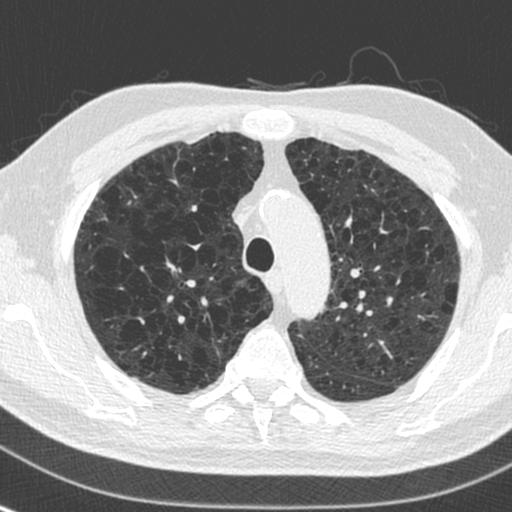
Chest CT (low-dose screening protocol), one axial image; baseline annual screen; lung window (W 1500 / L -600 HU); 512 × 512 image matrix, field of view 305 × 305 mm. Male, age 73 years at enrolment. Current smoker at enrolment.
Lesion marked by an expert reader, bounding box [x1, y1, x2, y2] px = [155, 251, 201, 287]. Screening reader's record for this exam: no non-calcified nodule ≥4 mm recorded. Participant outcome: lung cancer diagnosed 446 days after this screen (after the second annual screen) — squamous cell carcinoma, NOS, right upper lobe, stage IA (AJCC 6th edition), 10 mm at pathology.